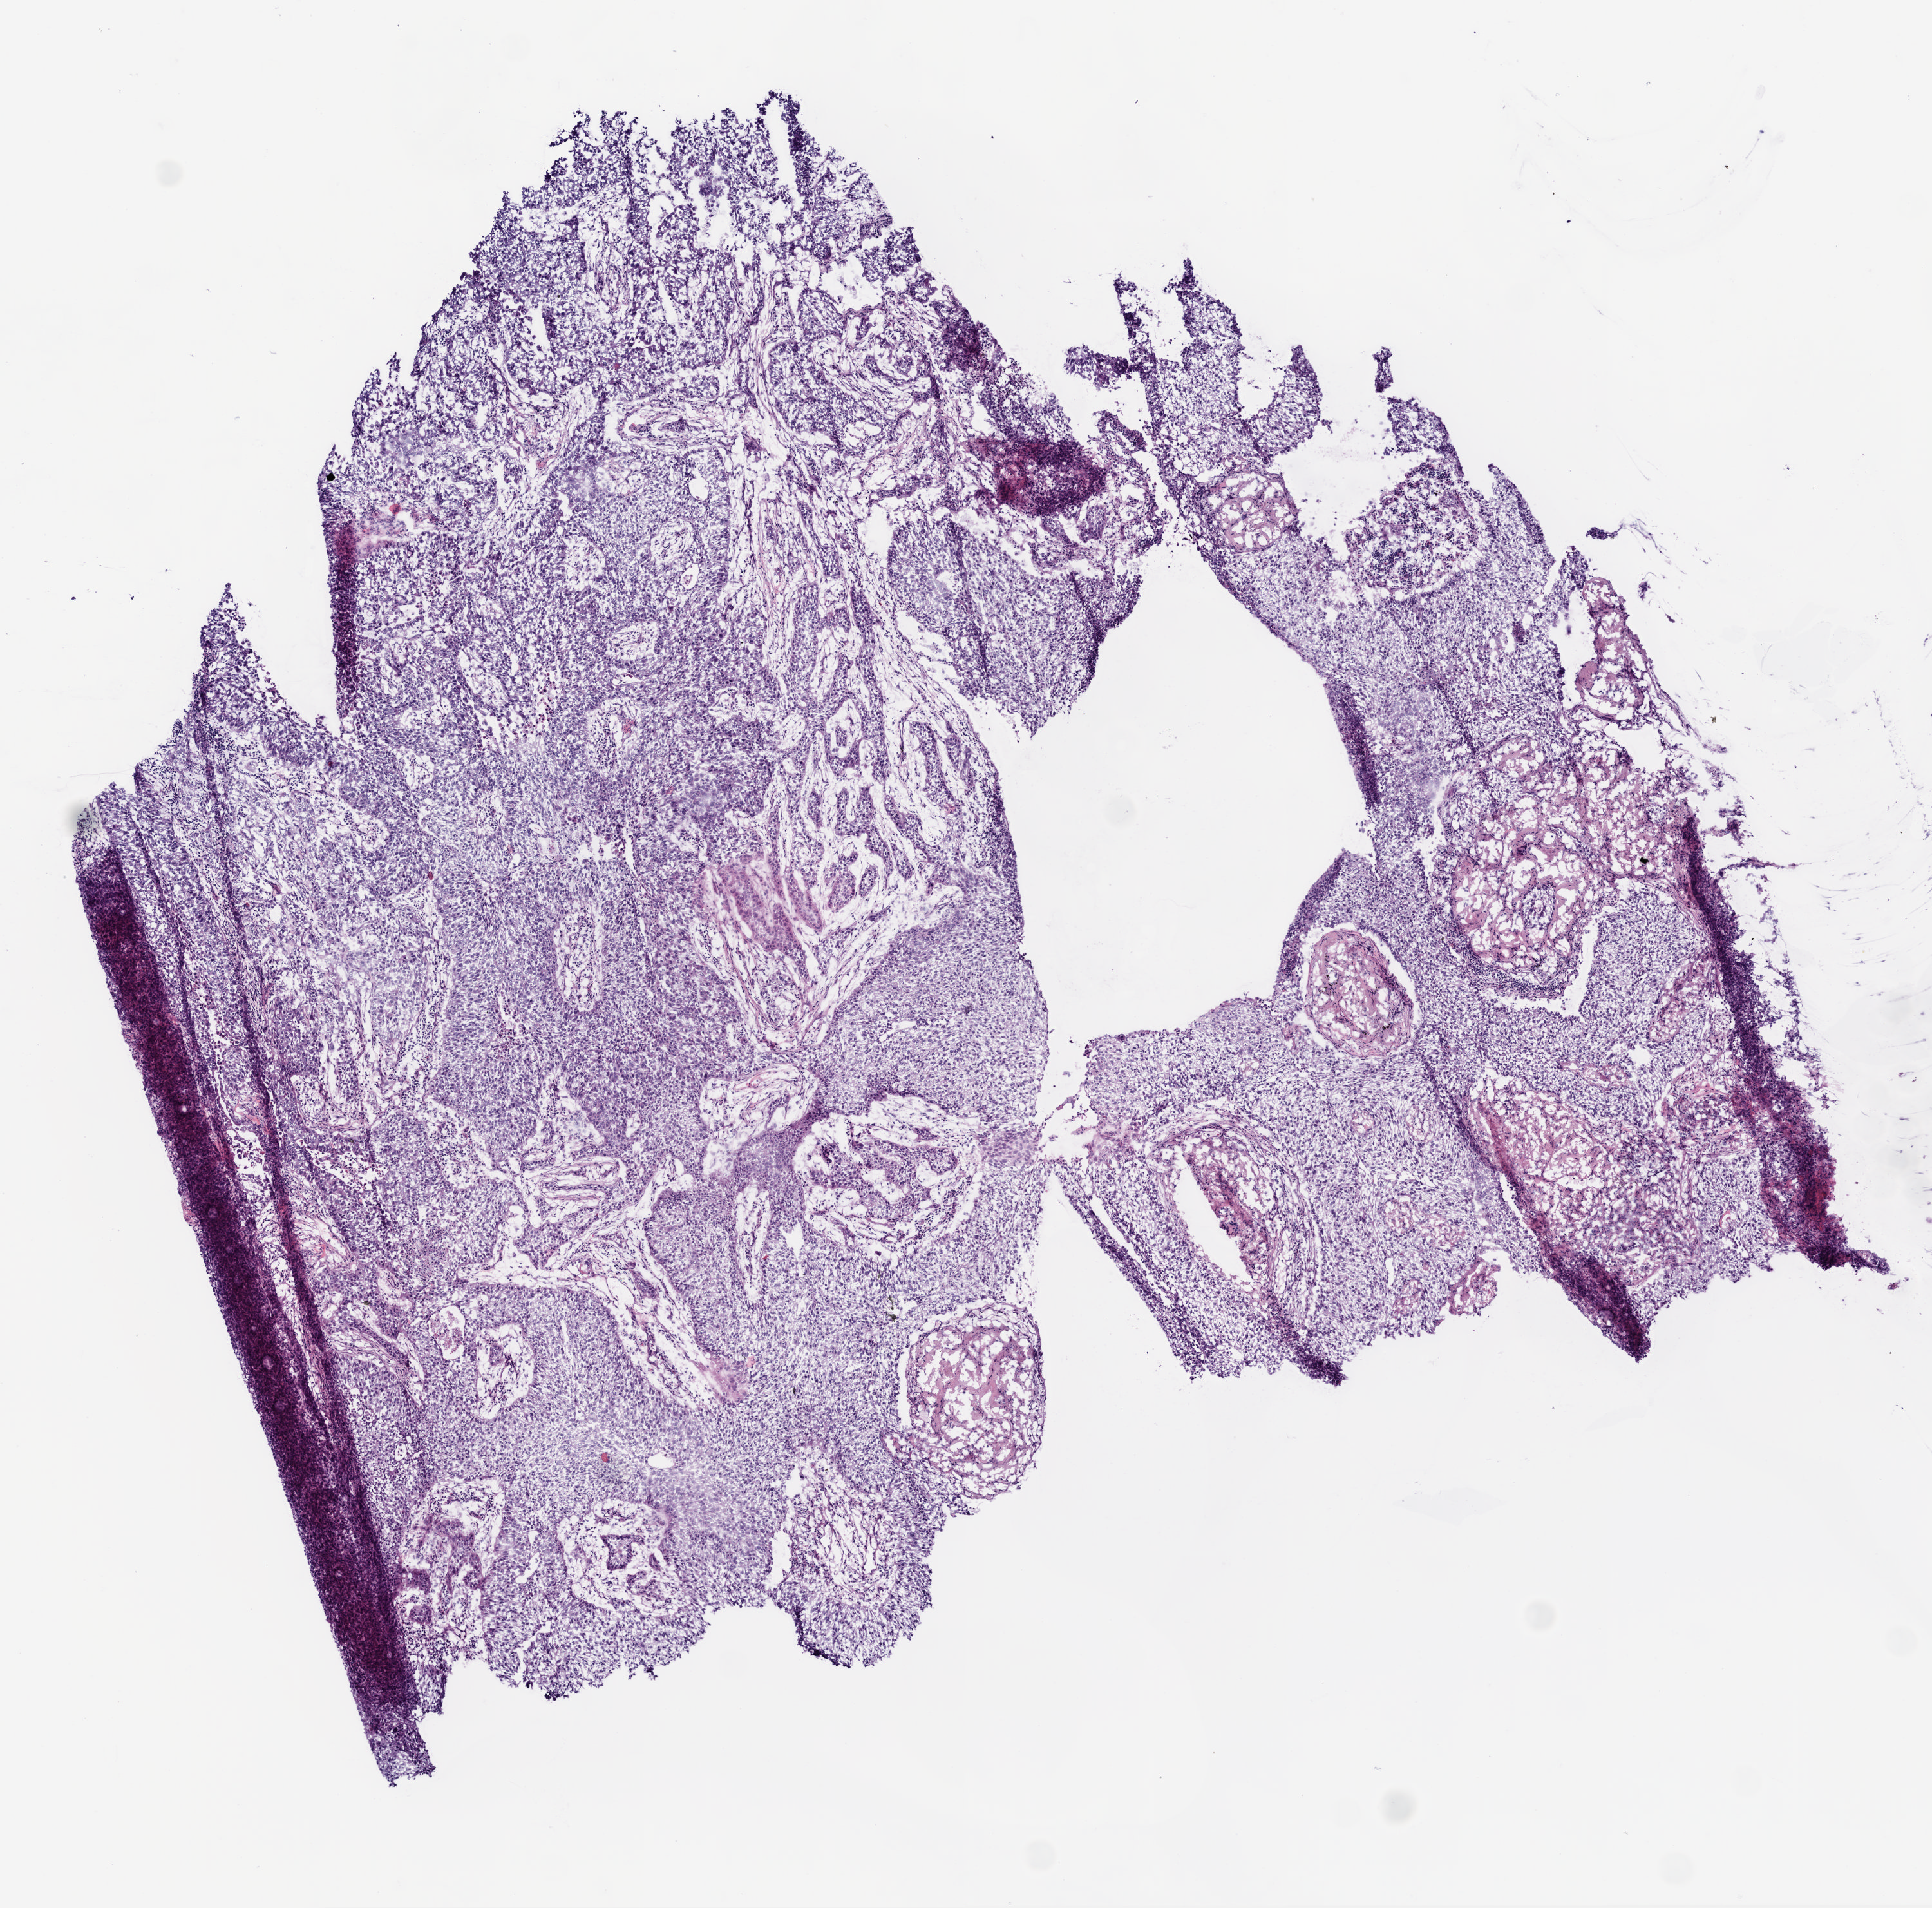
Whole-slide histology image, Hematoxylin and eosin (H&E) stained, shown as a low-resolution overview of the whole scanned area (about 6.0 x 5.9 mm). Frozen section from the top of the tissue portion. Sample: primary tumour, lung. Male, age 73 years at initial diagnosis. Composition of this section per pathologist review: tumour cells 83%, tumour nuclei 90%, normal cells 0%, stromal cells 15%, necrosis 2%. Inflammatory infiltration, as recorded: lymphocyte infiltration 2%.
TNM: T4 N1 M1. AJCC pathologic stage: IV. Pathologic diagnosis: Squamous cell carcinoma, NOS.